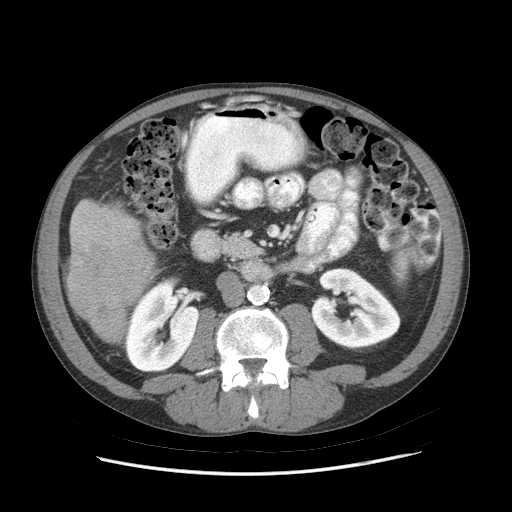
Contrast-enhanced abdominal CT (liver protocol), one axial slice. Position 19 of 89 along the scan axis. Reconstruction kernel STANDARD. 140 kVp. Soft-tissue window (W 400 / L 40 HU). 2.5 mm slice thickness. 512 × 512 image matrix, field of view 380 × 380 mm. Case-level facts recorded for this patient, not image findings: diagnosis: hepatocellular carcinoma (patient treated with transarterial chemoembolisation; whether this scan precedes or follows treatment is not stated here); TNM stage (as recorded): Stage-IIIB; Child-Pugh class: A; tumour differentiation: moderately differentiated; tumour nodularity: multinodular.
Annotated regions visible in this slice (semi-automatically segmented with operator editing):
- liver parenchyma outside the tumour (the mass and vessels are separate outlines, so this box may not span the whole liver): bounding box <66,198,154,342> (left, top, right, bottom; pixels)
- mass: <67,239,154,332>